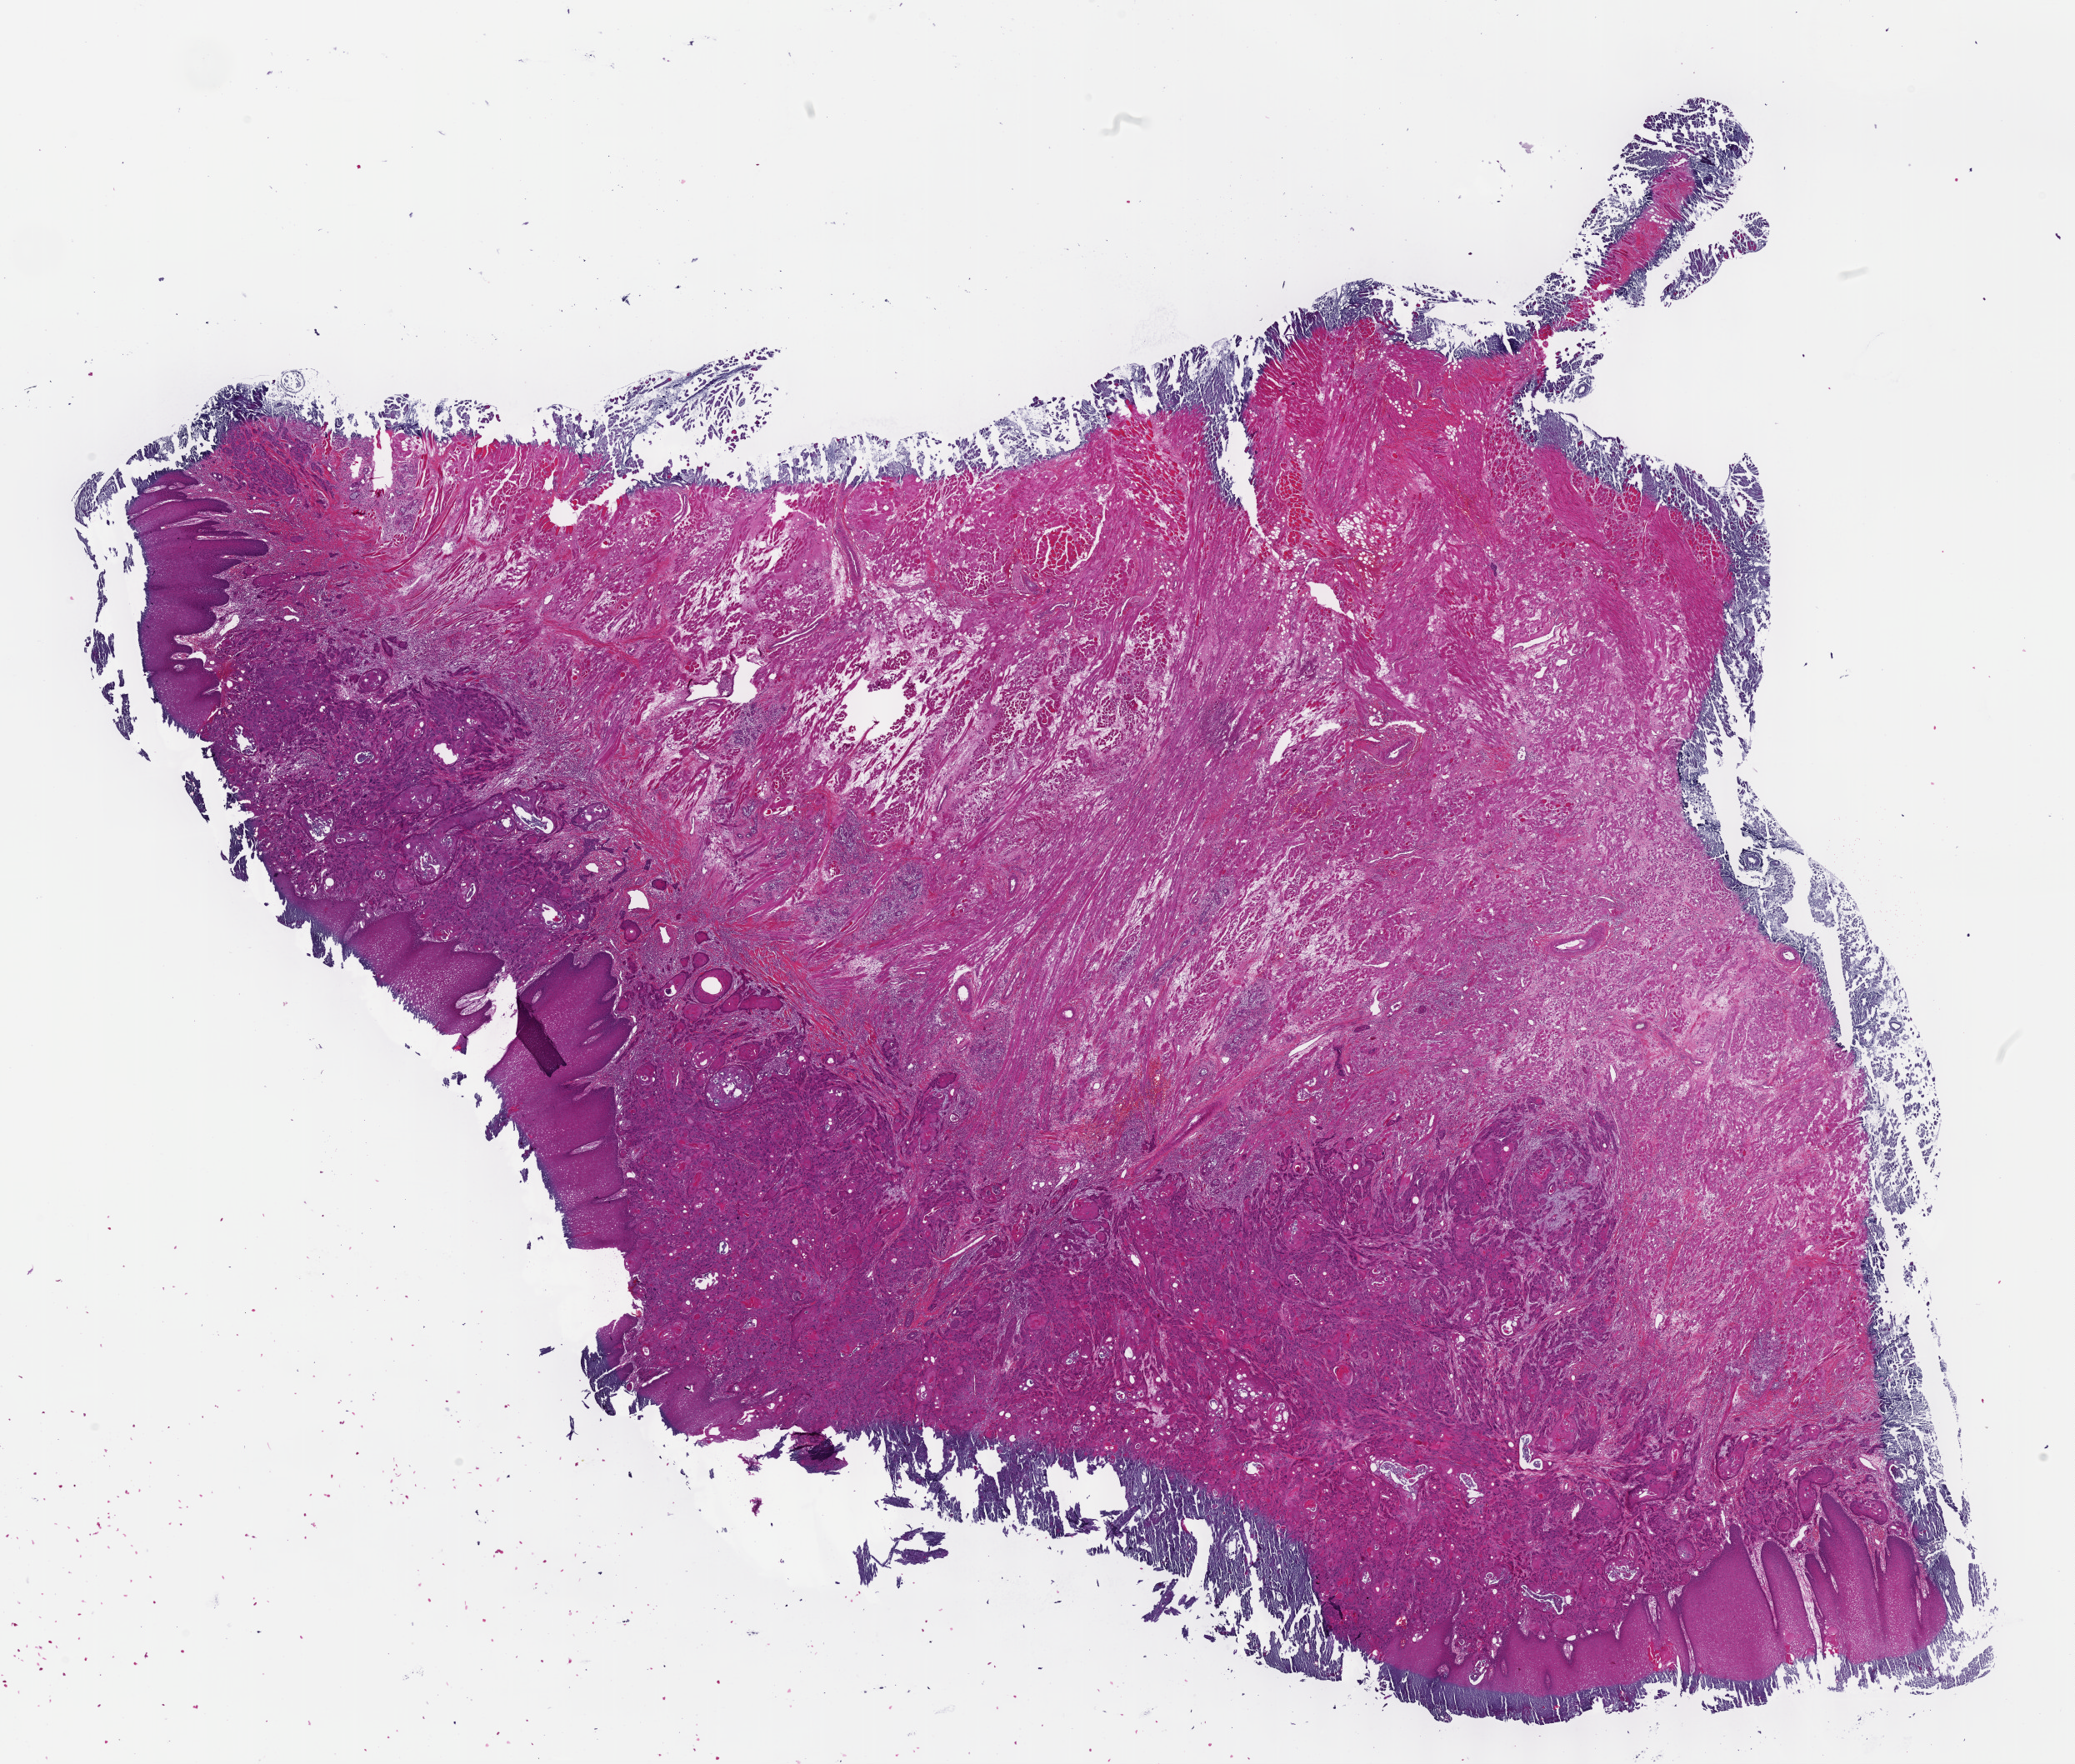
Digitized H&E-stained tissue section (whole slide), low-resolution overview of the scanned area, about 20.1 x 17.1 mm (slide scanned at 40x), formalin-fixed paraffin-embedded (FFPE) diagnostic section, head and neck, primary tumour sample. Female patient; age at initial diagnosis 32 years. Histologic grade: G2 (moderately differentiated).
Histologic diagnosis: Squamous cell carcinoma, NOS (tongue, NOS). AJCC pathologic stage: IVA (7th edition).